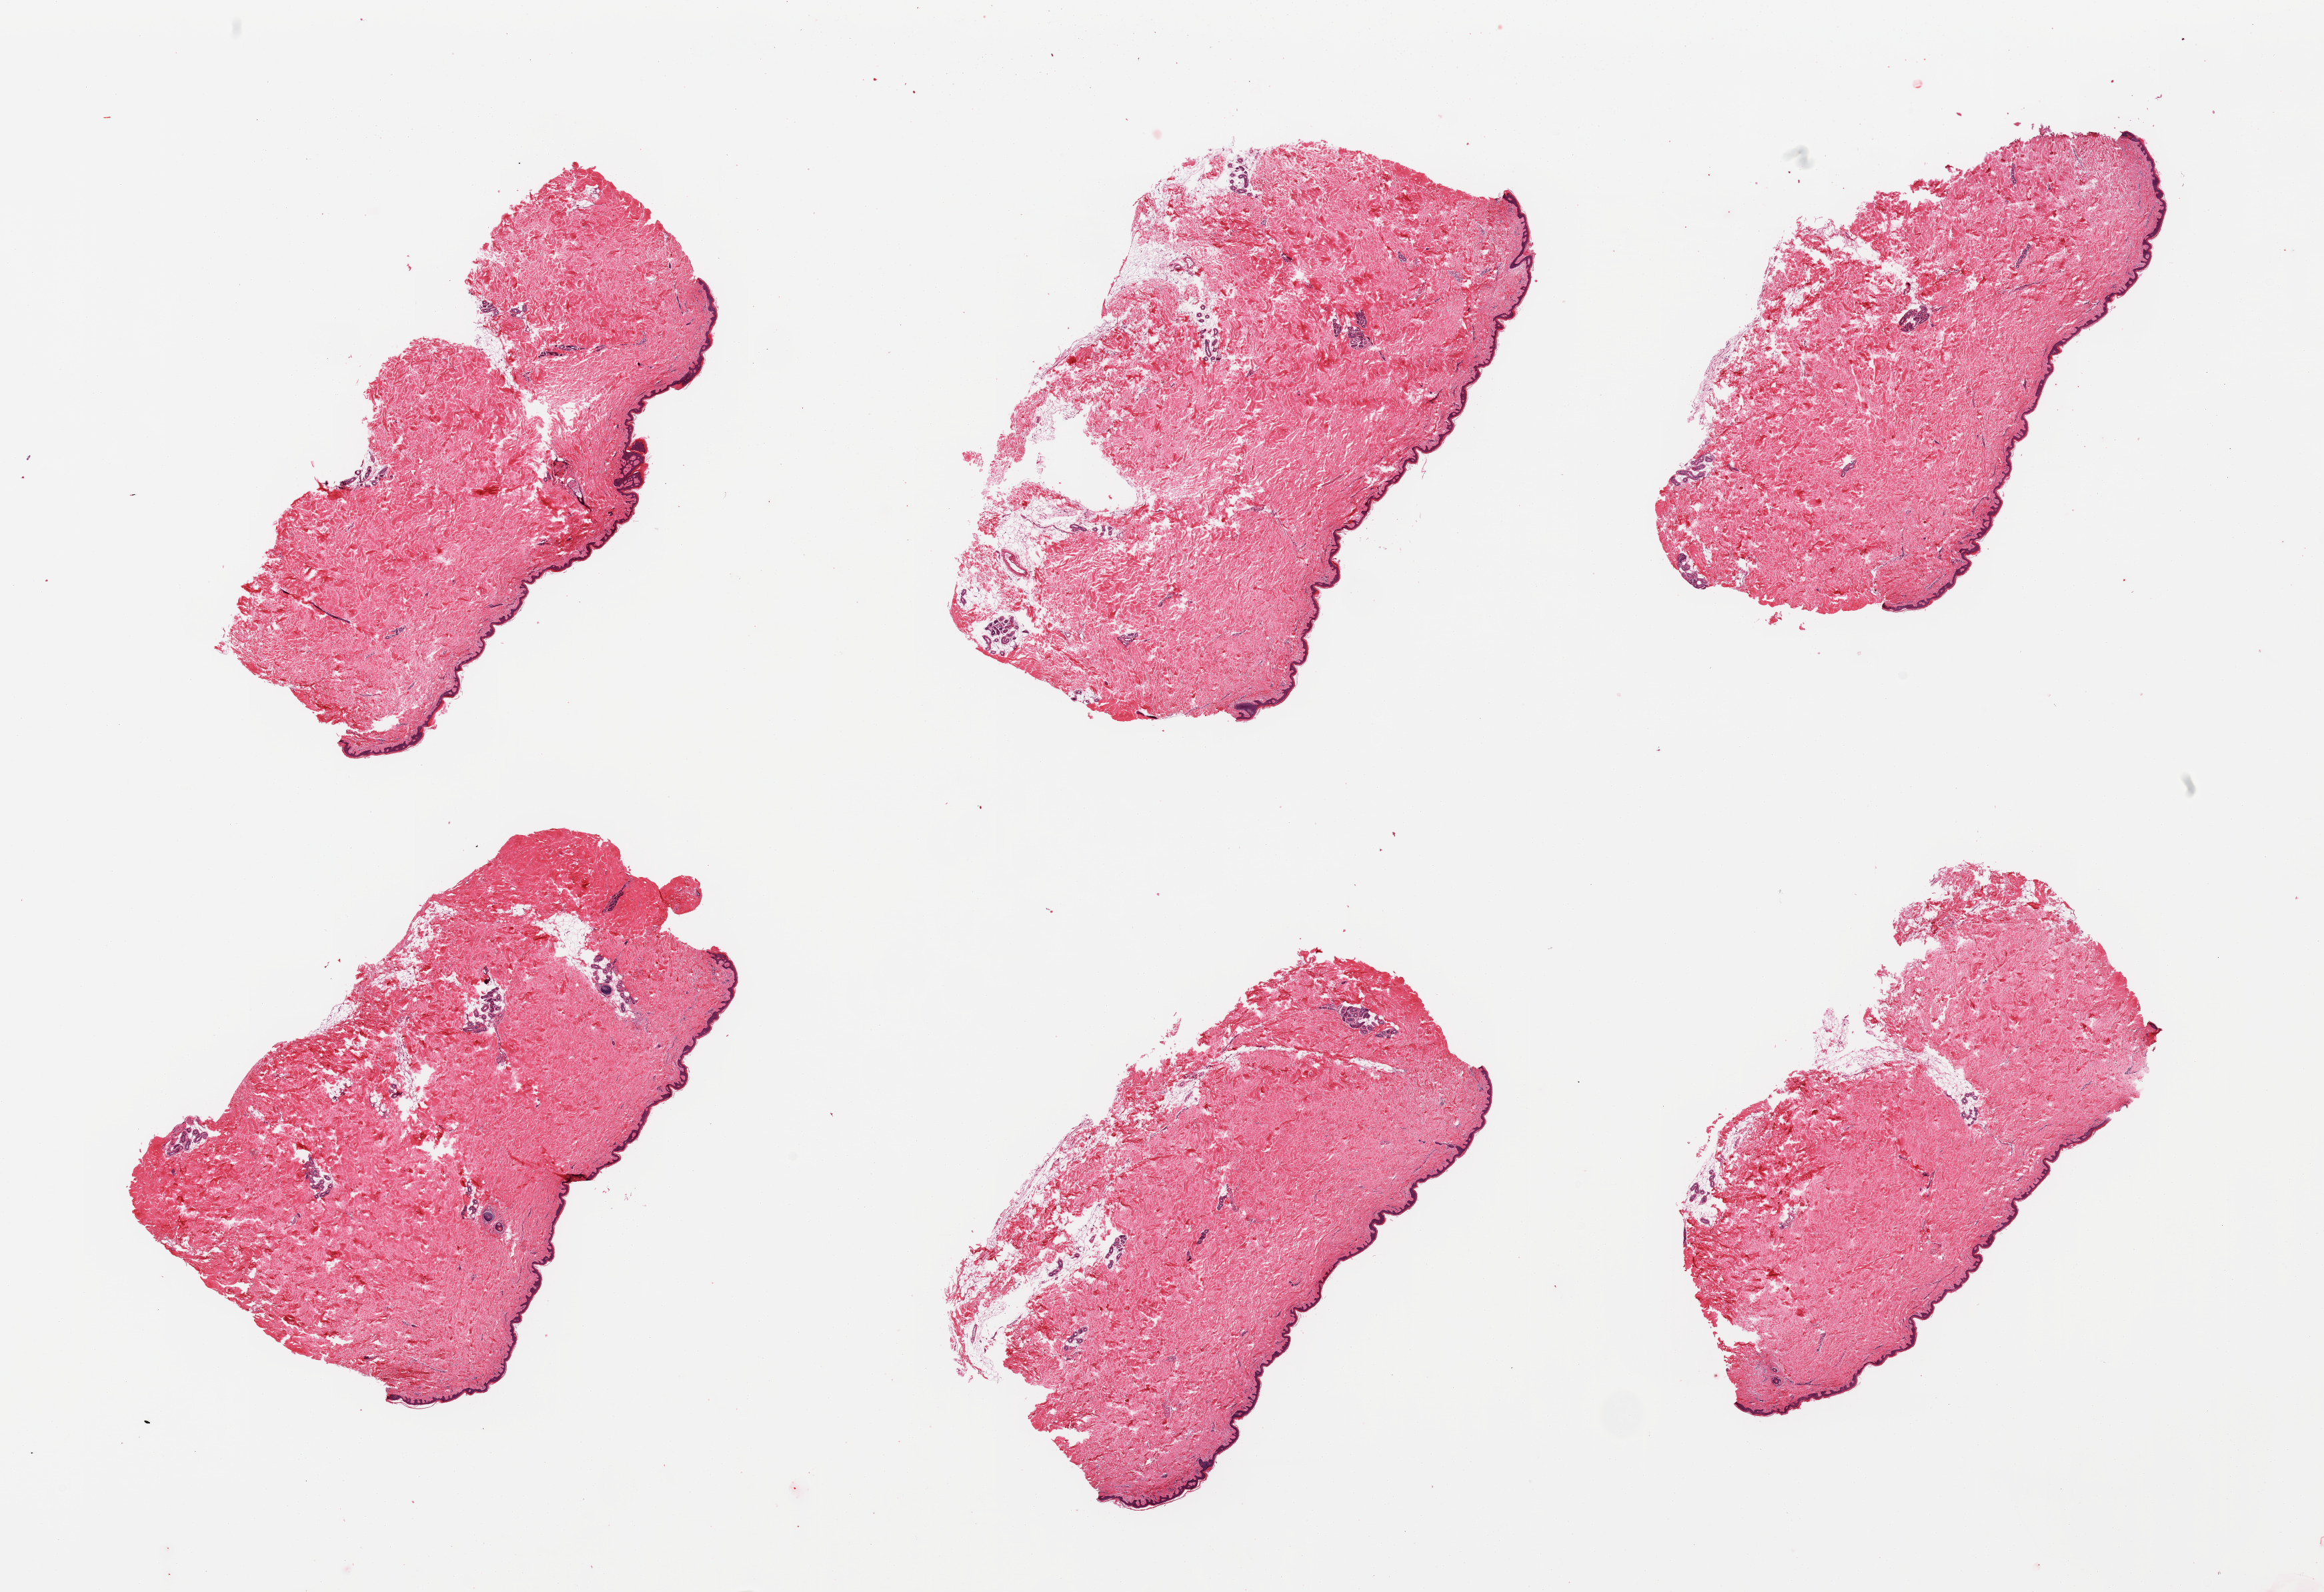
Whole-slide image, H&E stain, a low-resolution overview of the entire scanned area, about 27.6 x 18.9 mm. PAXgene-fixed paraffin-embedded (PFPE) section. Target tissue: skin of suprapubic region. Tissue donor sample. Donor: female.
* review note (as recorded): 6 pieces; well trimmed, includes trivial component of internal fat